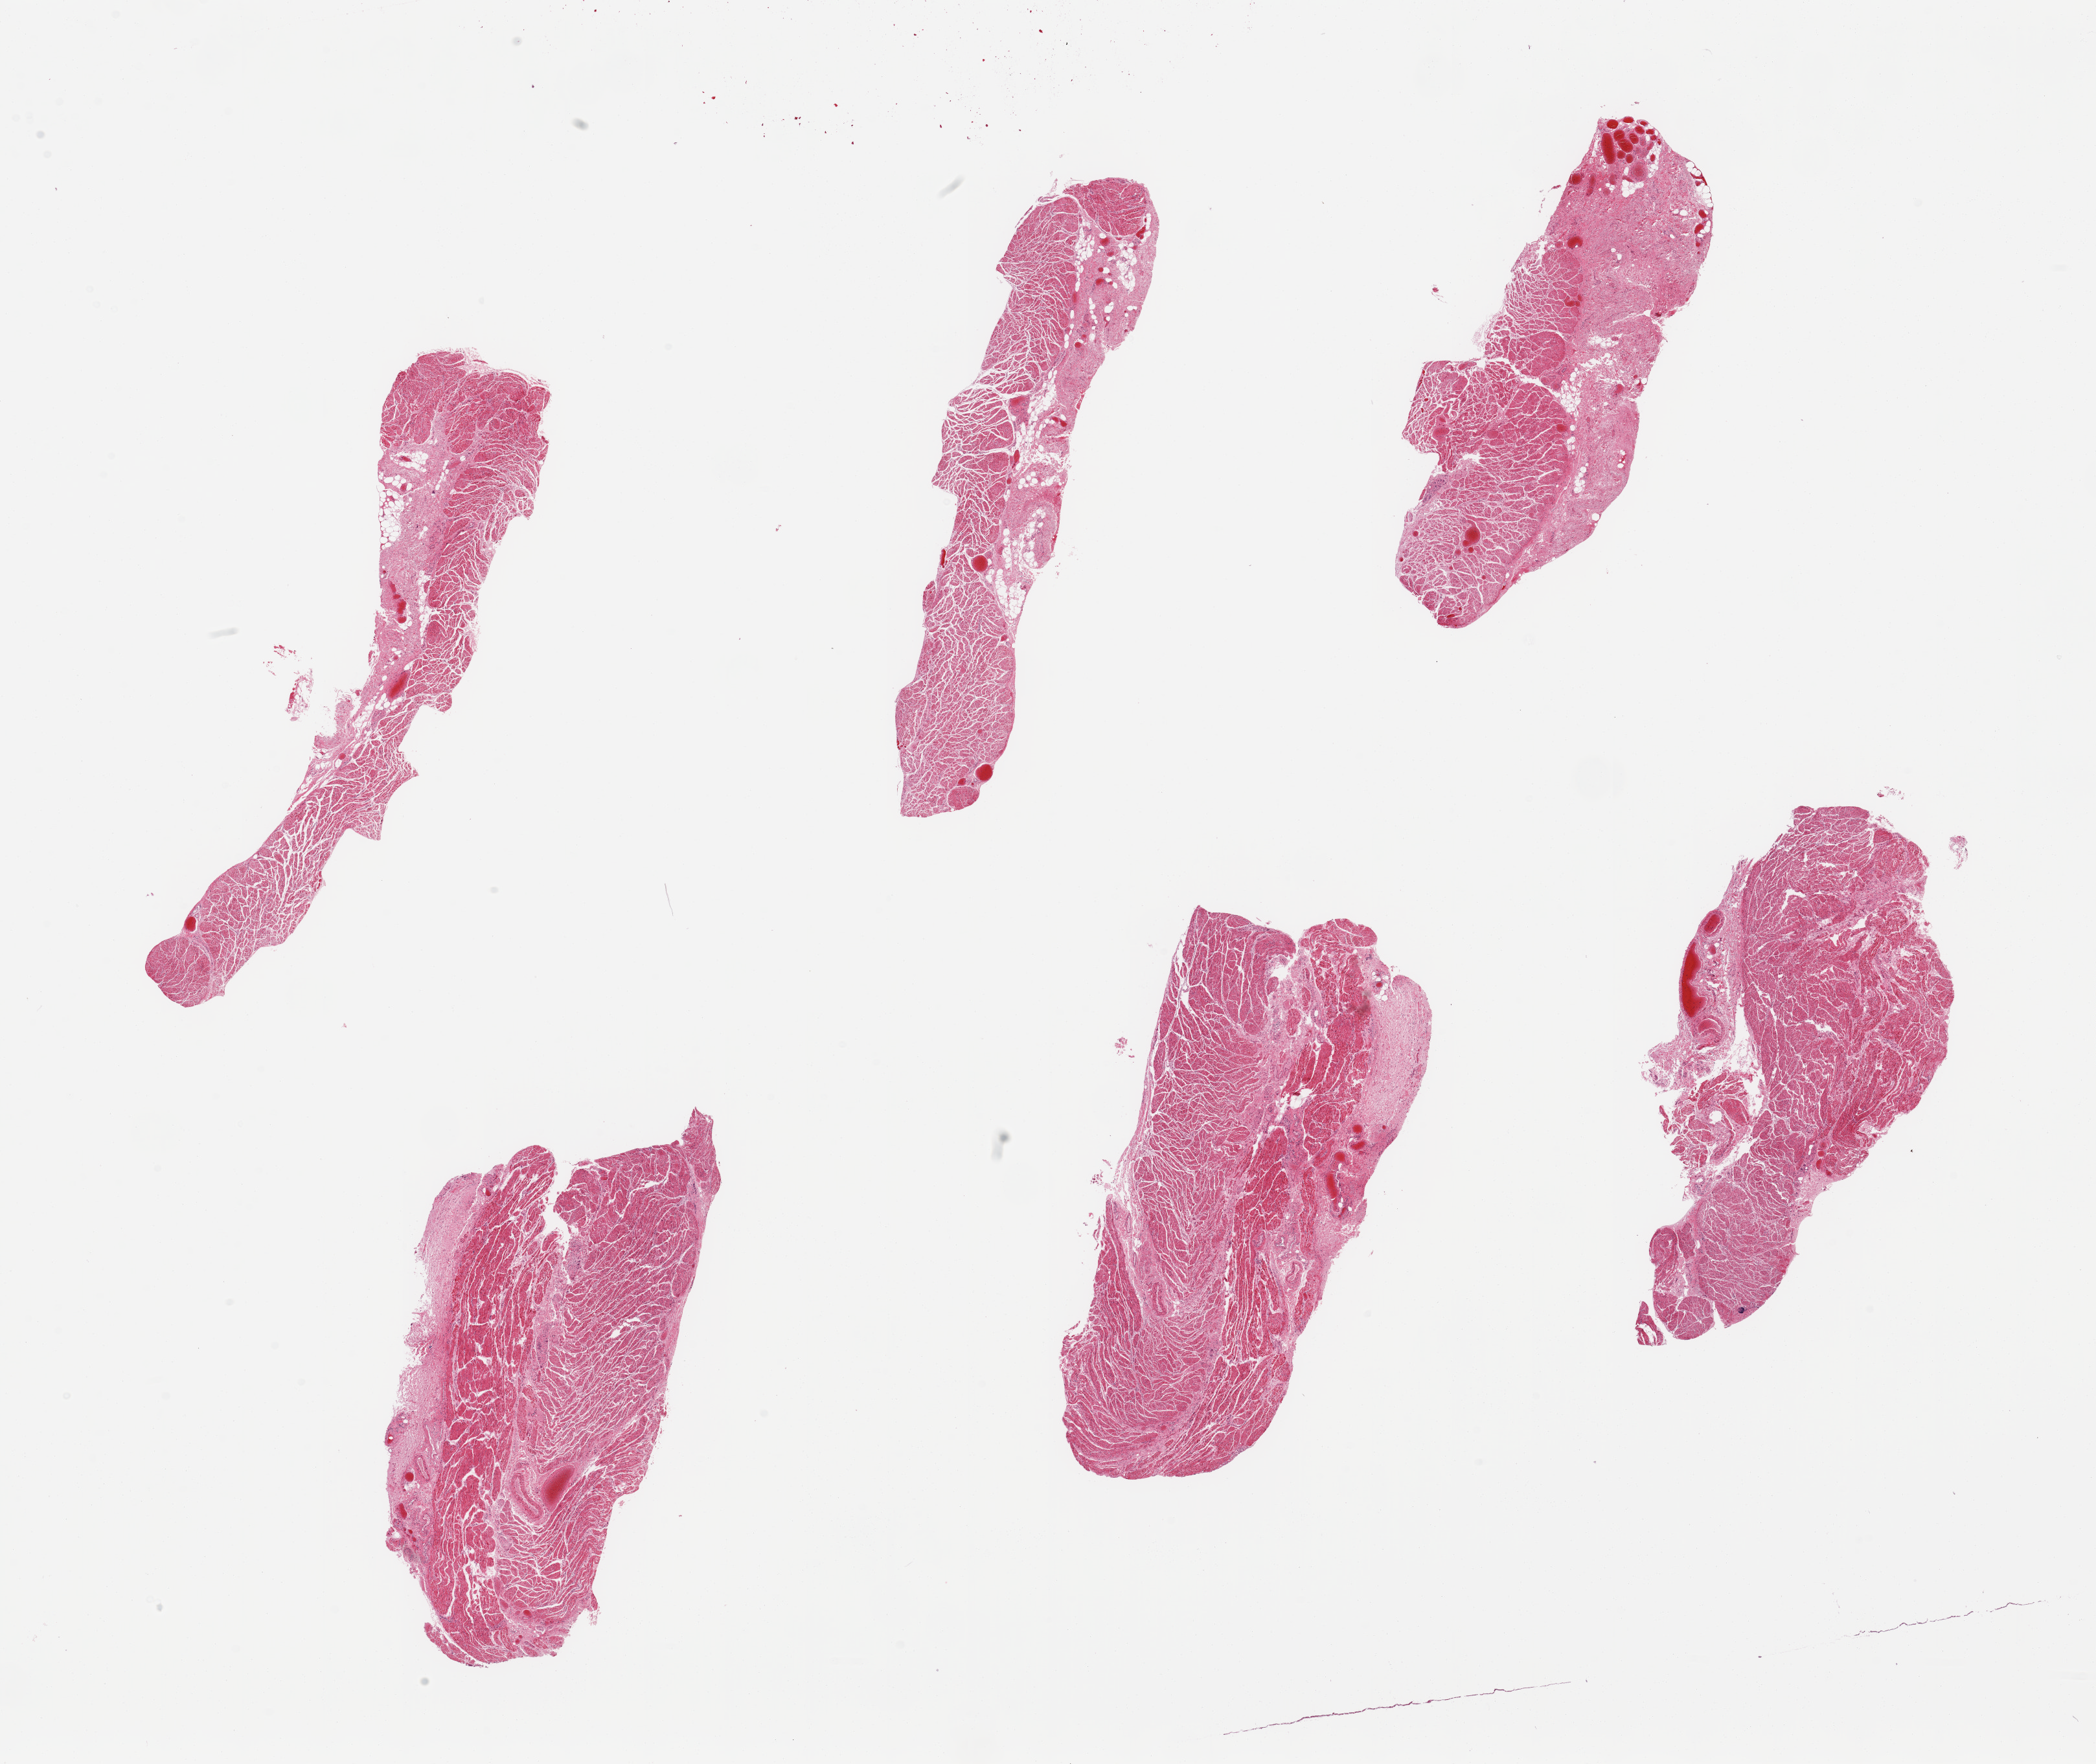
H&E whole-slide image, whole scanned area (about 25.6 x 21.5 mm) shown as a low-resolution overview, PAXgene-fixed paraffin-embedded (PFPE) section, sampled site (target tissue): esophageal muscle, donor tissue sample.
Review note (as recorded): 6 pieces; well dissected except for up to 1.3mm submucosal stroma.